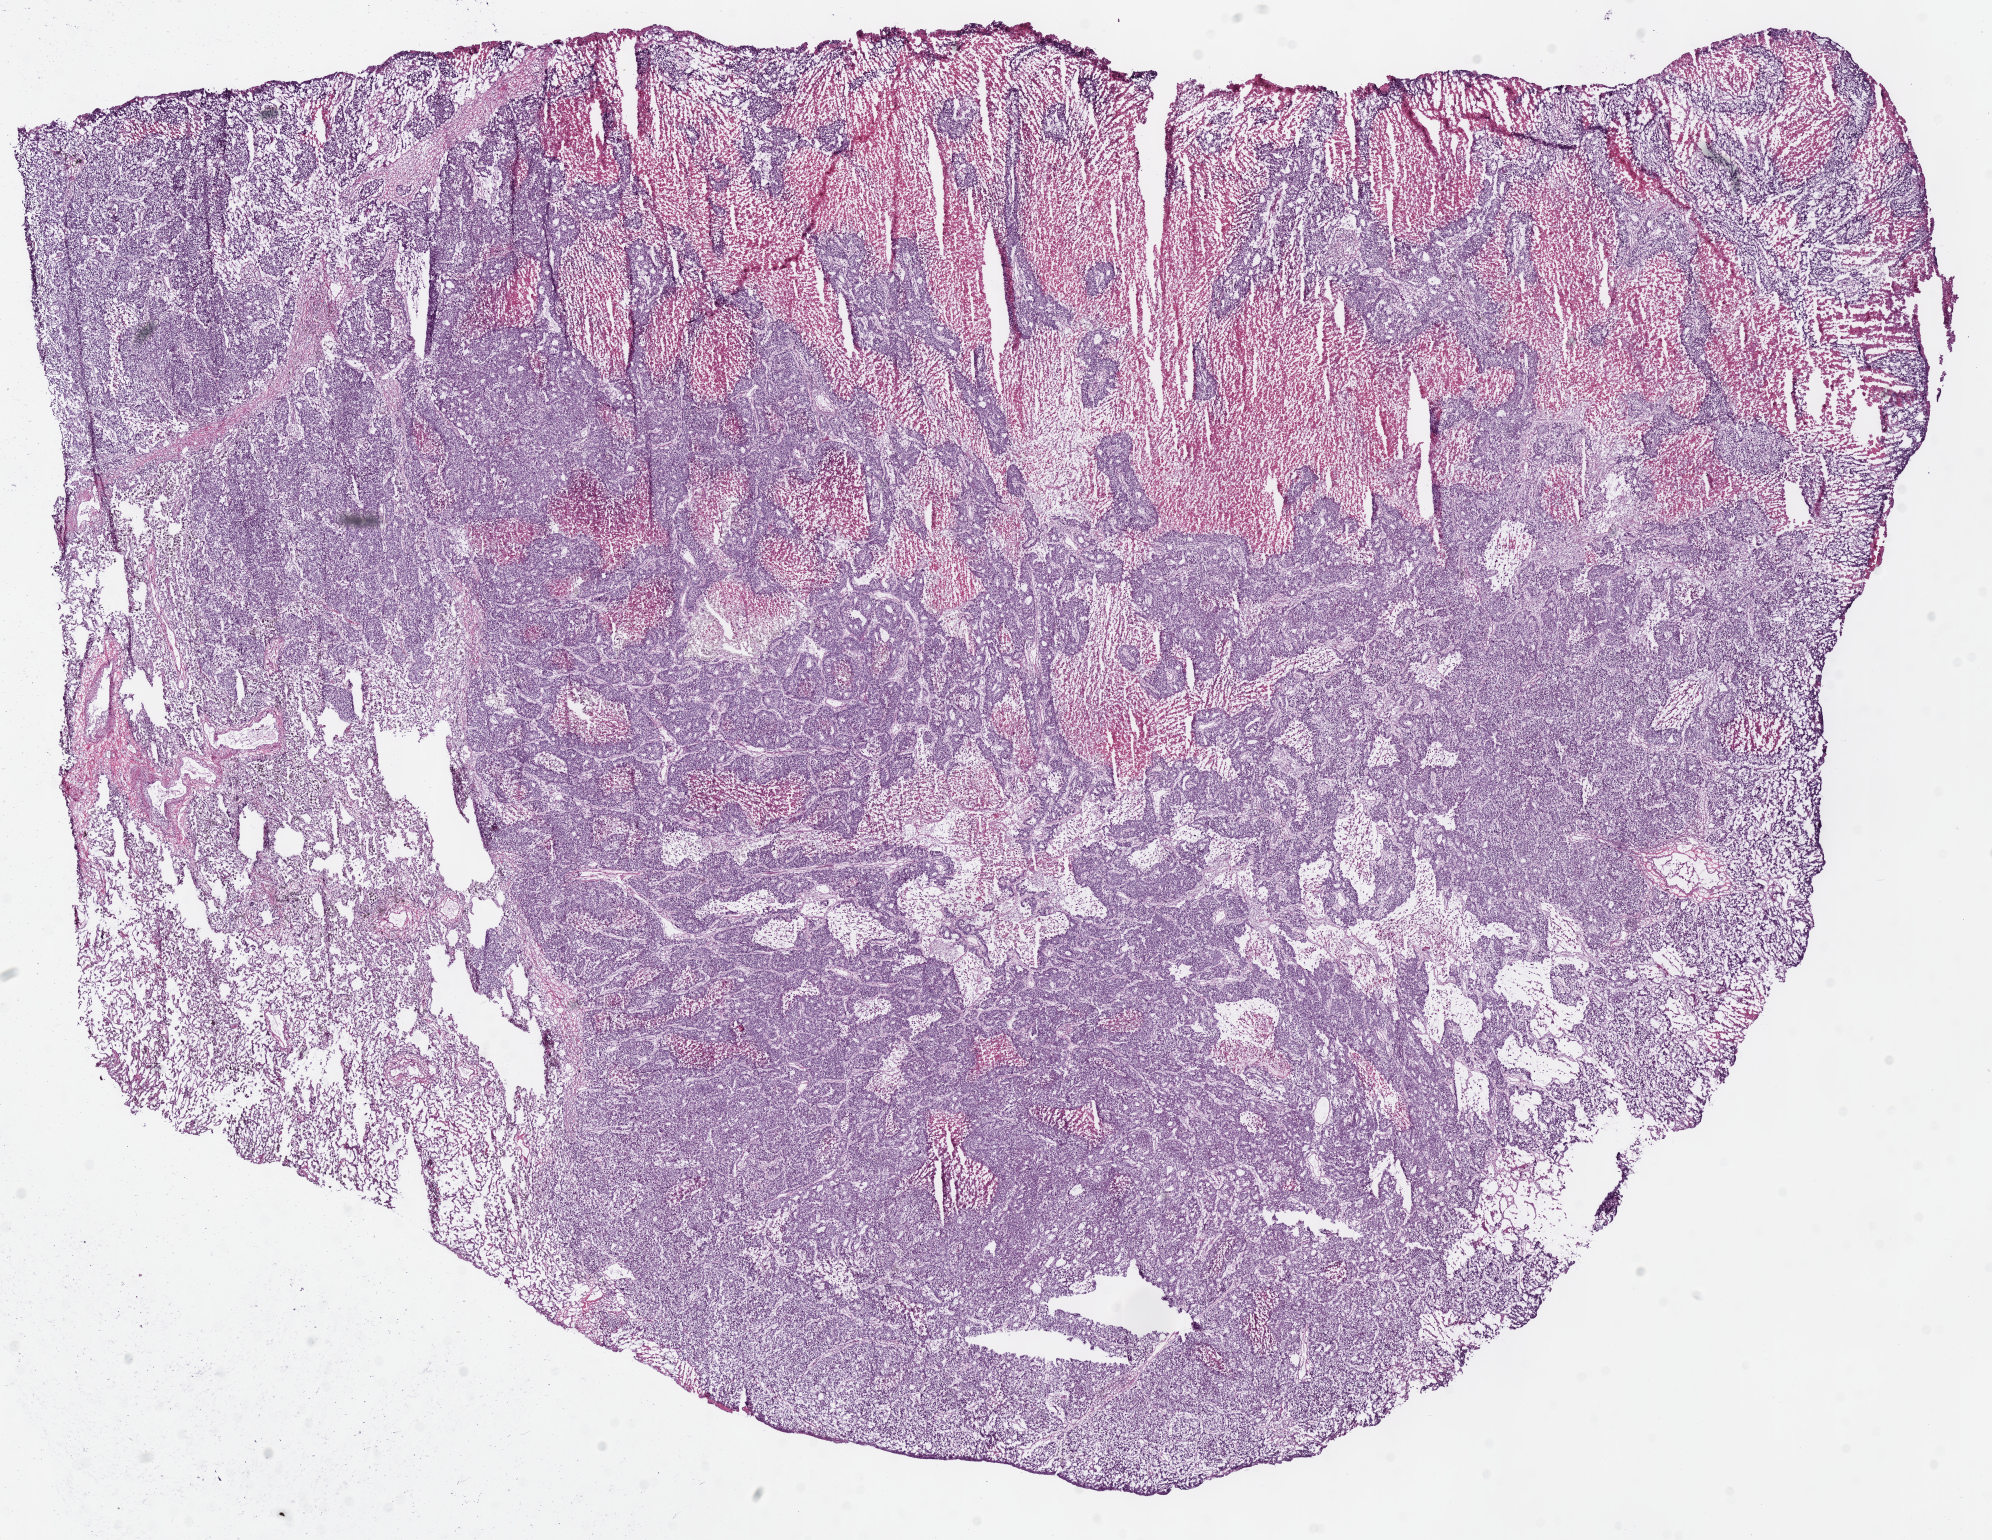
H&E-stained whole-slide image — shown as a low-resolution overview of the whole scanned area (about 15.7 x 12.1 mm, from a 40x scan). Frozen section from the bottom of the tissue portion. Sample: primary tumour, lung. Patient: male, age at initial diagnosis 61 years. Slide review estimates, as recorded: tumour cells 70%, tumour nuclei 85%, normal cells 5%, stromal cells 5%, necrosis 20%.
- AJCC pathologic stage: IIB
- diagnosis: Acinar cell carcinoma (upper lobe, lung)